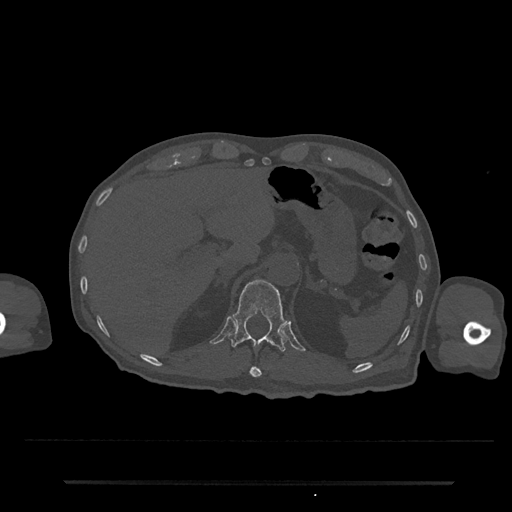
CT including the spine, one axial slice. Position 204 of 797 along the scan axis. Reconstruction kernel Br40s/3. 120 kVp. Bone window (W 1800 / L 400 HU). 0.5 mm slice thickness. 512 × 512 image matrix. Male patient, age 74 years. From the clinical record (not read from this slice): primary cancer: prostate.
Structures marked on this image (semi-automatically segmented with operator editing):
- T11 vertebra: box from (x=249, y=366) to (x=262, y=378) px
- T12 vertebra: (x=228, y=280)–(x=287, y=352)